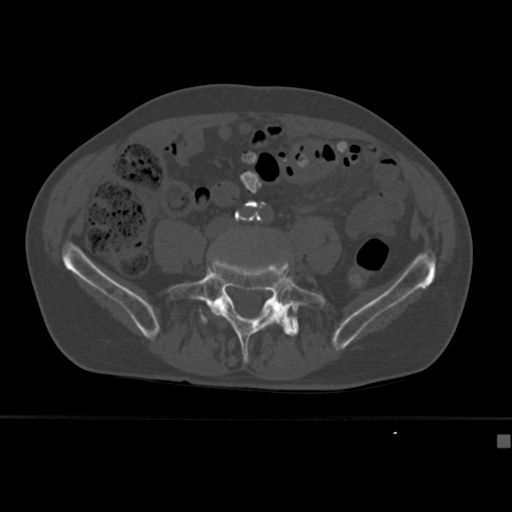
CT including the spine, one axial slice; position 90 of 430 along the scan axis; reconstruction kernel Br40s; 120 kVp; bone window (W 1800 / L 400 HU); 512 × 512 image matrix, field of view 337 × 337 mm. Patient: male, 64 years. Case-level facts recorded for this patient, not image findings: primary cancer: uterus; vertebrae with lytic lesions (as recorded): T1, T4, T5, T7, L5.
Annotated regions visible in this slice (semi-automatic segmentation, software-assisted and operator-edited):
- L4 vertebra: box from (x=212, y=310) to (x=217, y=316) px
- L5 vertebra: (x=168, y=259)–(x=327, y=364)